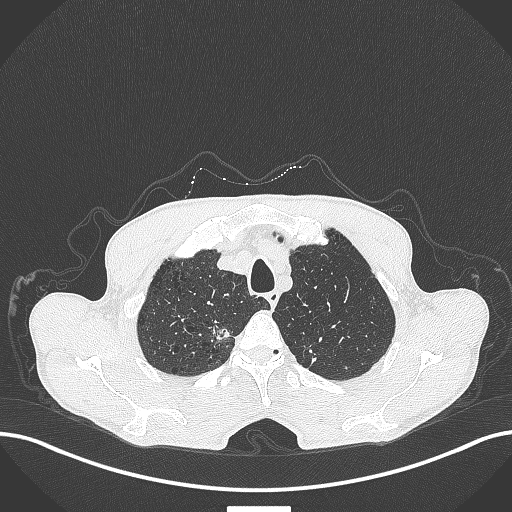
Chest CT, one axial slice; slice 367 of 445 in the series (ordered by position); 120 kVp; lung window (W 1500 / L -600 HU); 1 mm slice thickness; 512 × 512 image matrix, field of view 400 × 400 mm. Male patient, age 70 years. Case-level facts recorded for this patient, not image findings: clinical TNM (as recorded): T1a N0 M0; histopathological grade: G1-2.
Structures marked on this image (bounding box drawn by a radiologist):
- lung tumour (recorded histology: adenocarcinoma): bounding box [x1, y1, x2, y2] px = [205, 314, 235, 345]